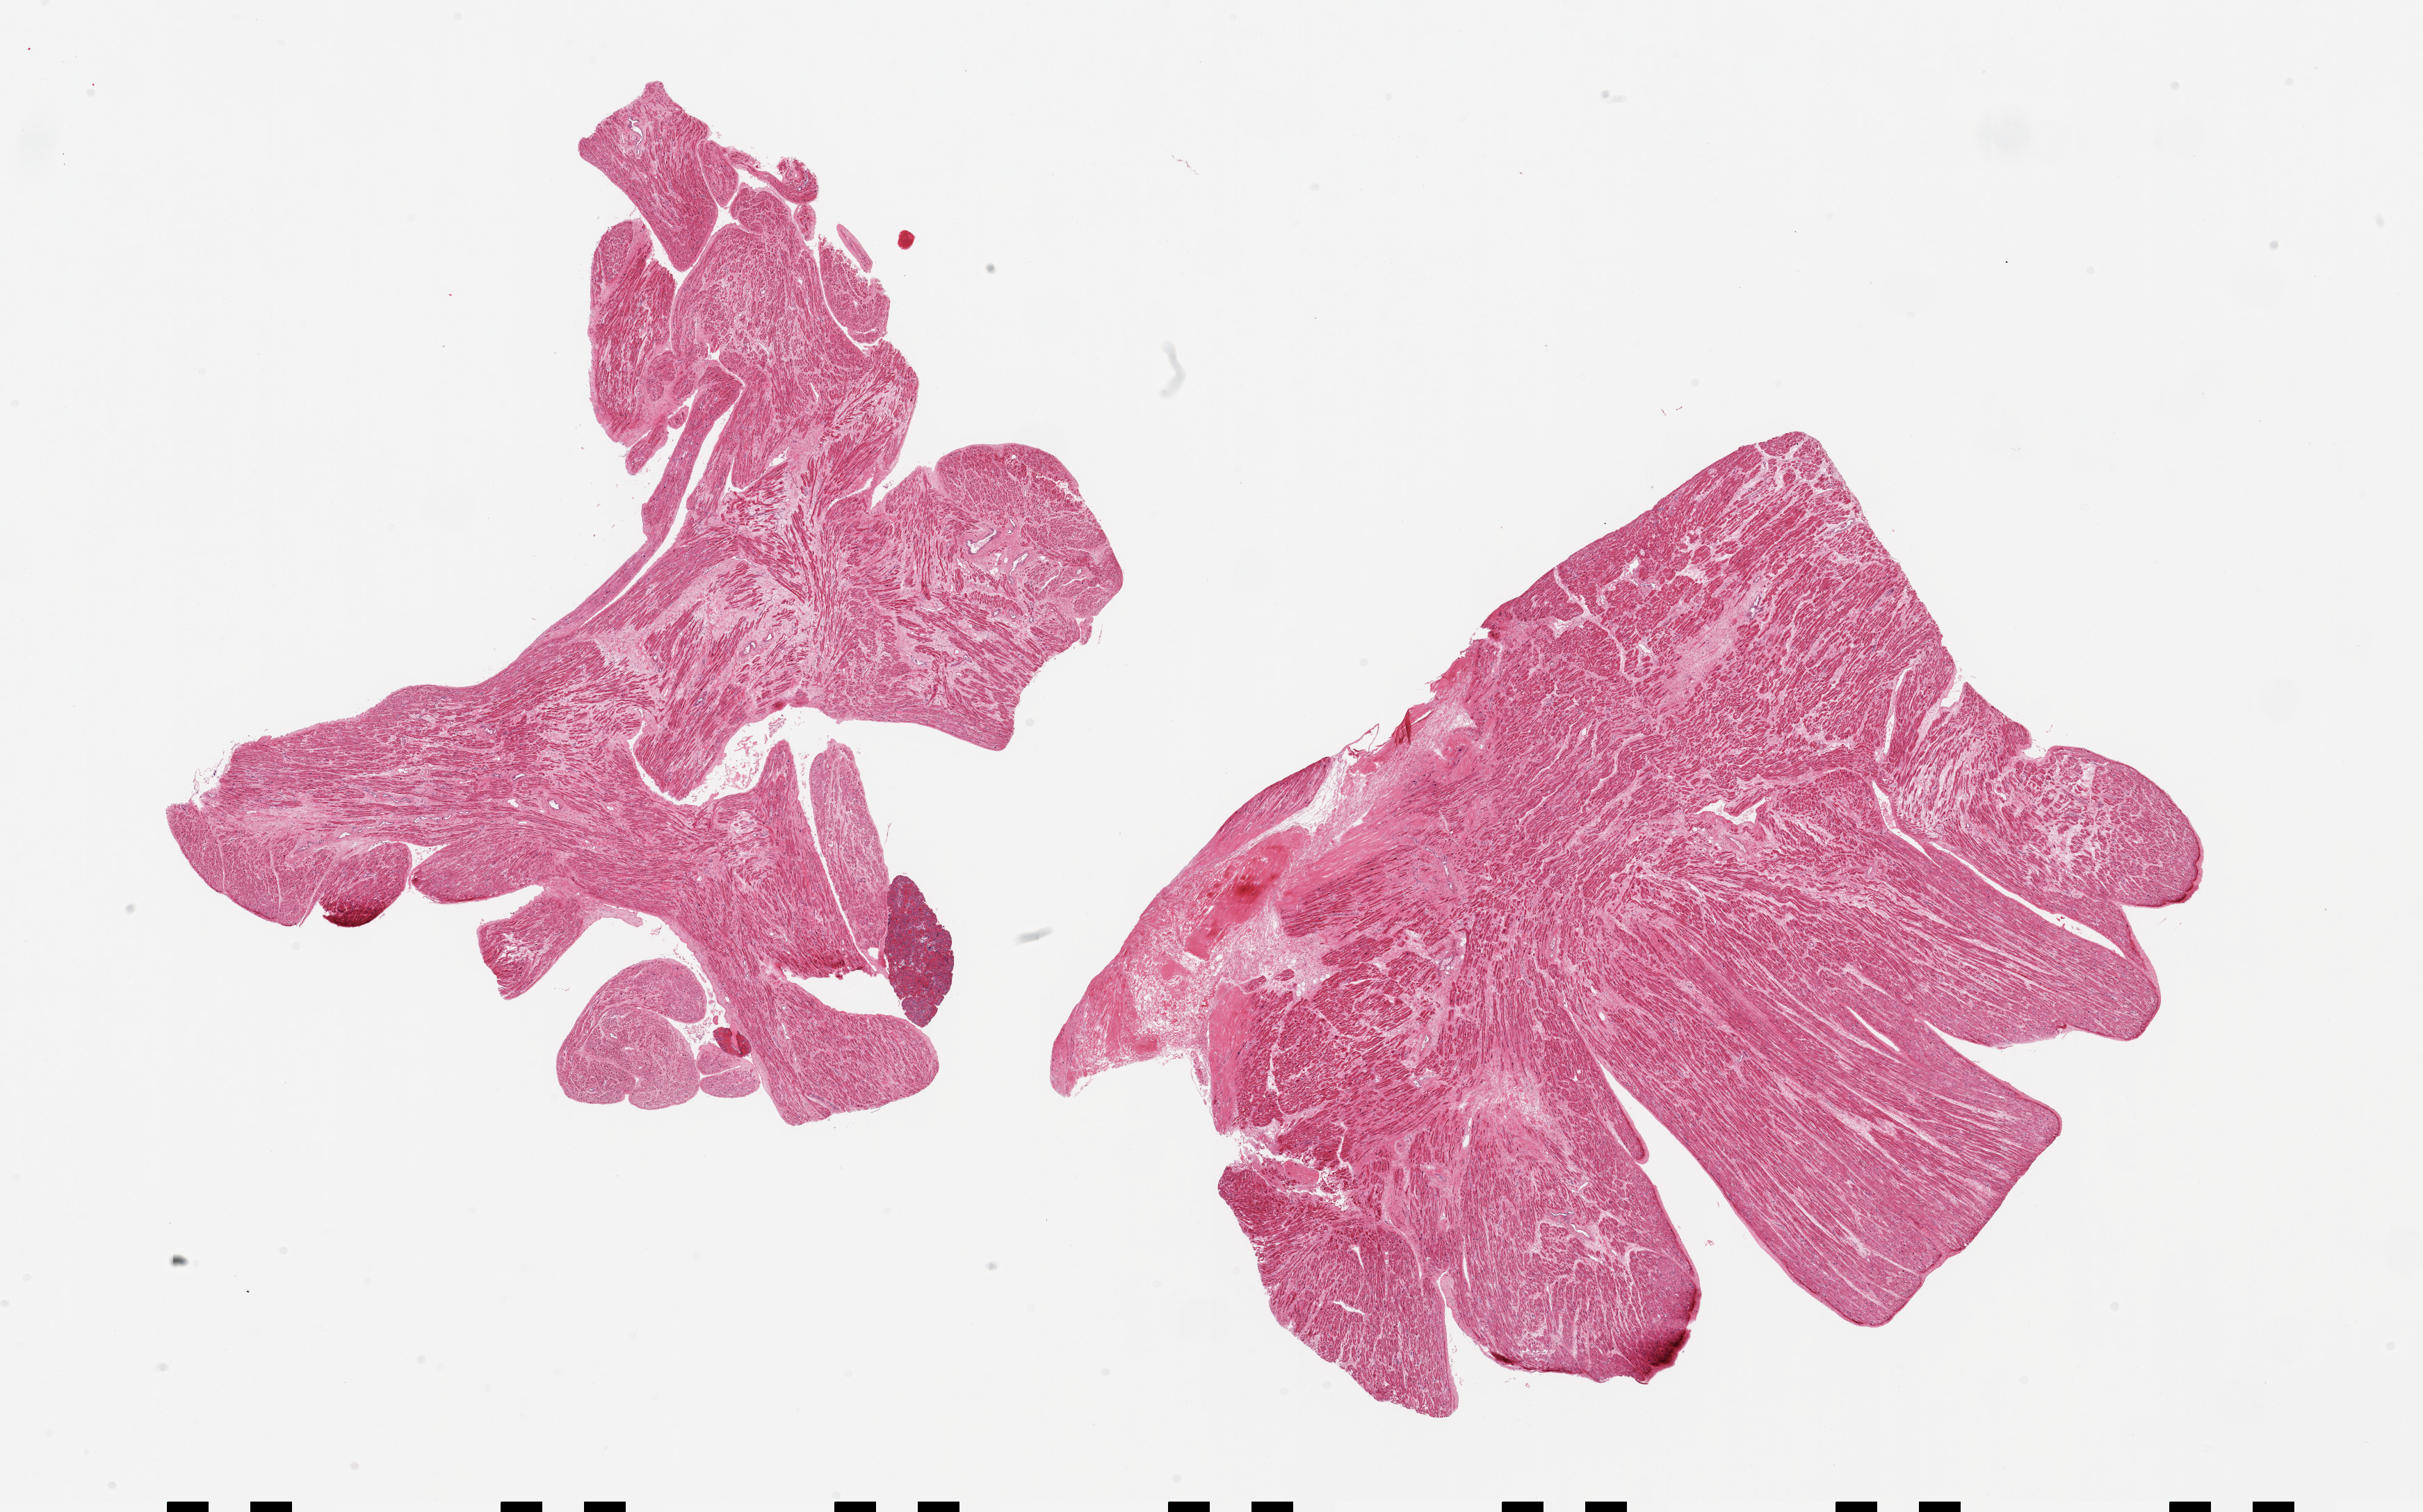
Hematoxylin and eosin (H&E) whole-slide image, brightfield — low-resolution overview of the scanned area, about 27.6 x 17.2 mm. PAXgene-fixed, paraffin-embedded tissue. Sampled site (target tissue): auricular appendage. Donor tissue sample. Male donor.
- review note (as recorded): 2 pieces, no abnormalities